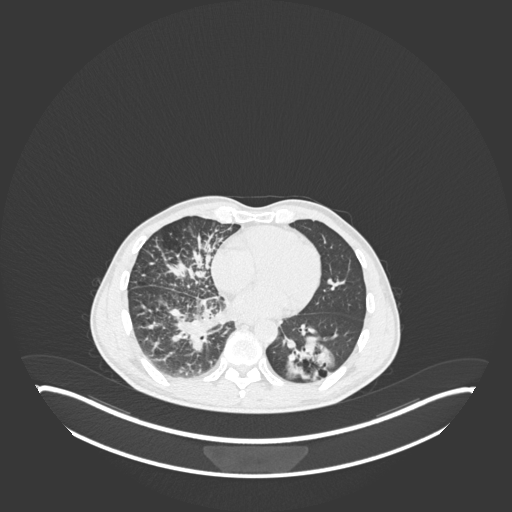
Chest CT, one axial slice; slice 93 of 237 in the series (ordered by position); lung window (W 1500 / L -600 HU); 1 mm slice thickness; 512 × 512 image matrix, field of view 500 × 500 mm. Male patient, age 49 years. From the clinical record (not read from this slice): clinical TNM (as recorded): T2b N1 M0.
Outlined on this slice (bounding box drawn by a radiologist):
- lung tumour (recorded histology: adenocarcinoma): bounding box (x1, y1, x2, y2) in pixels: (281, 328, 344, 383)